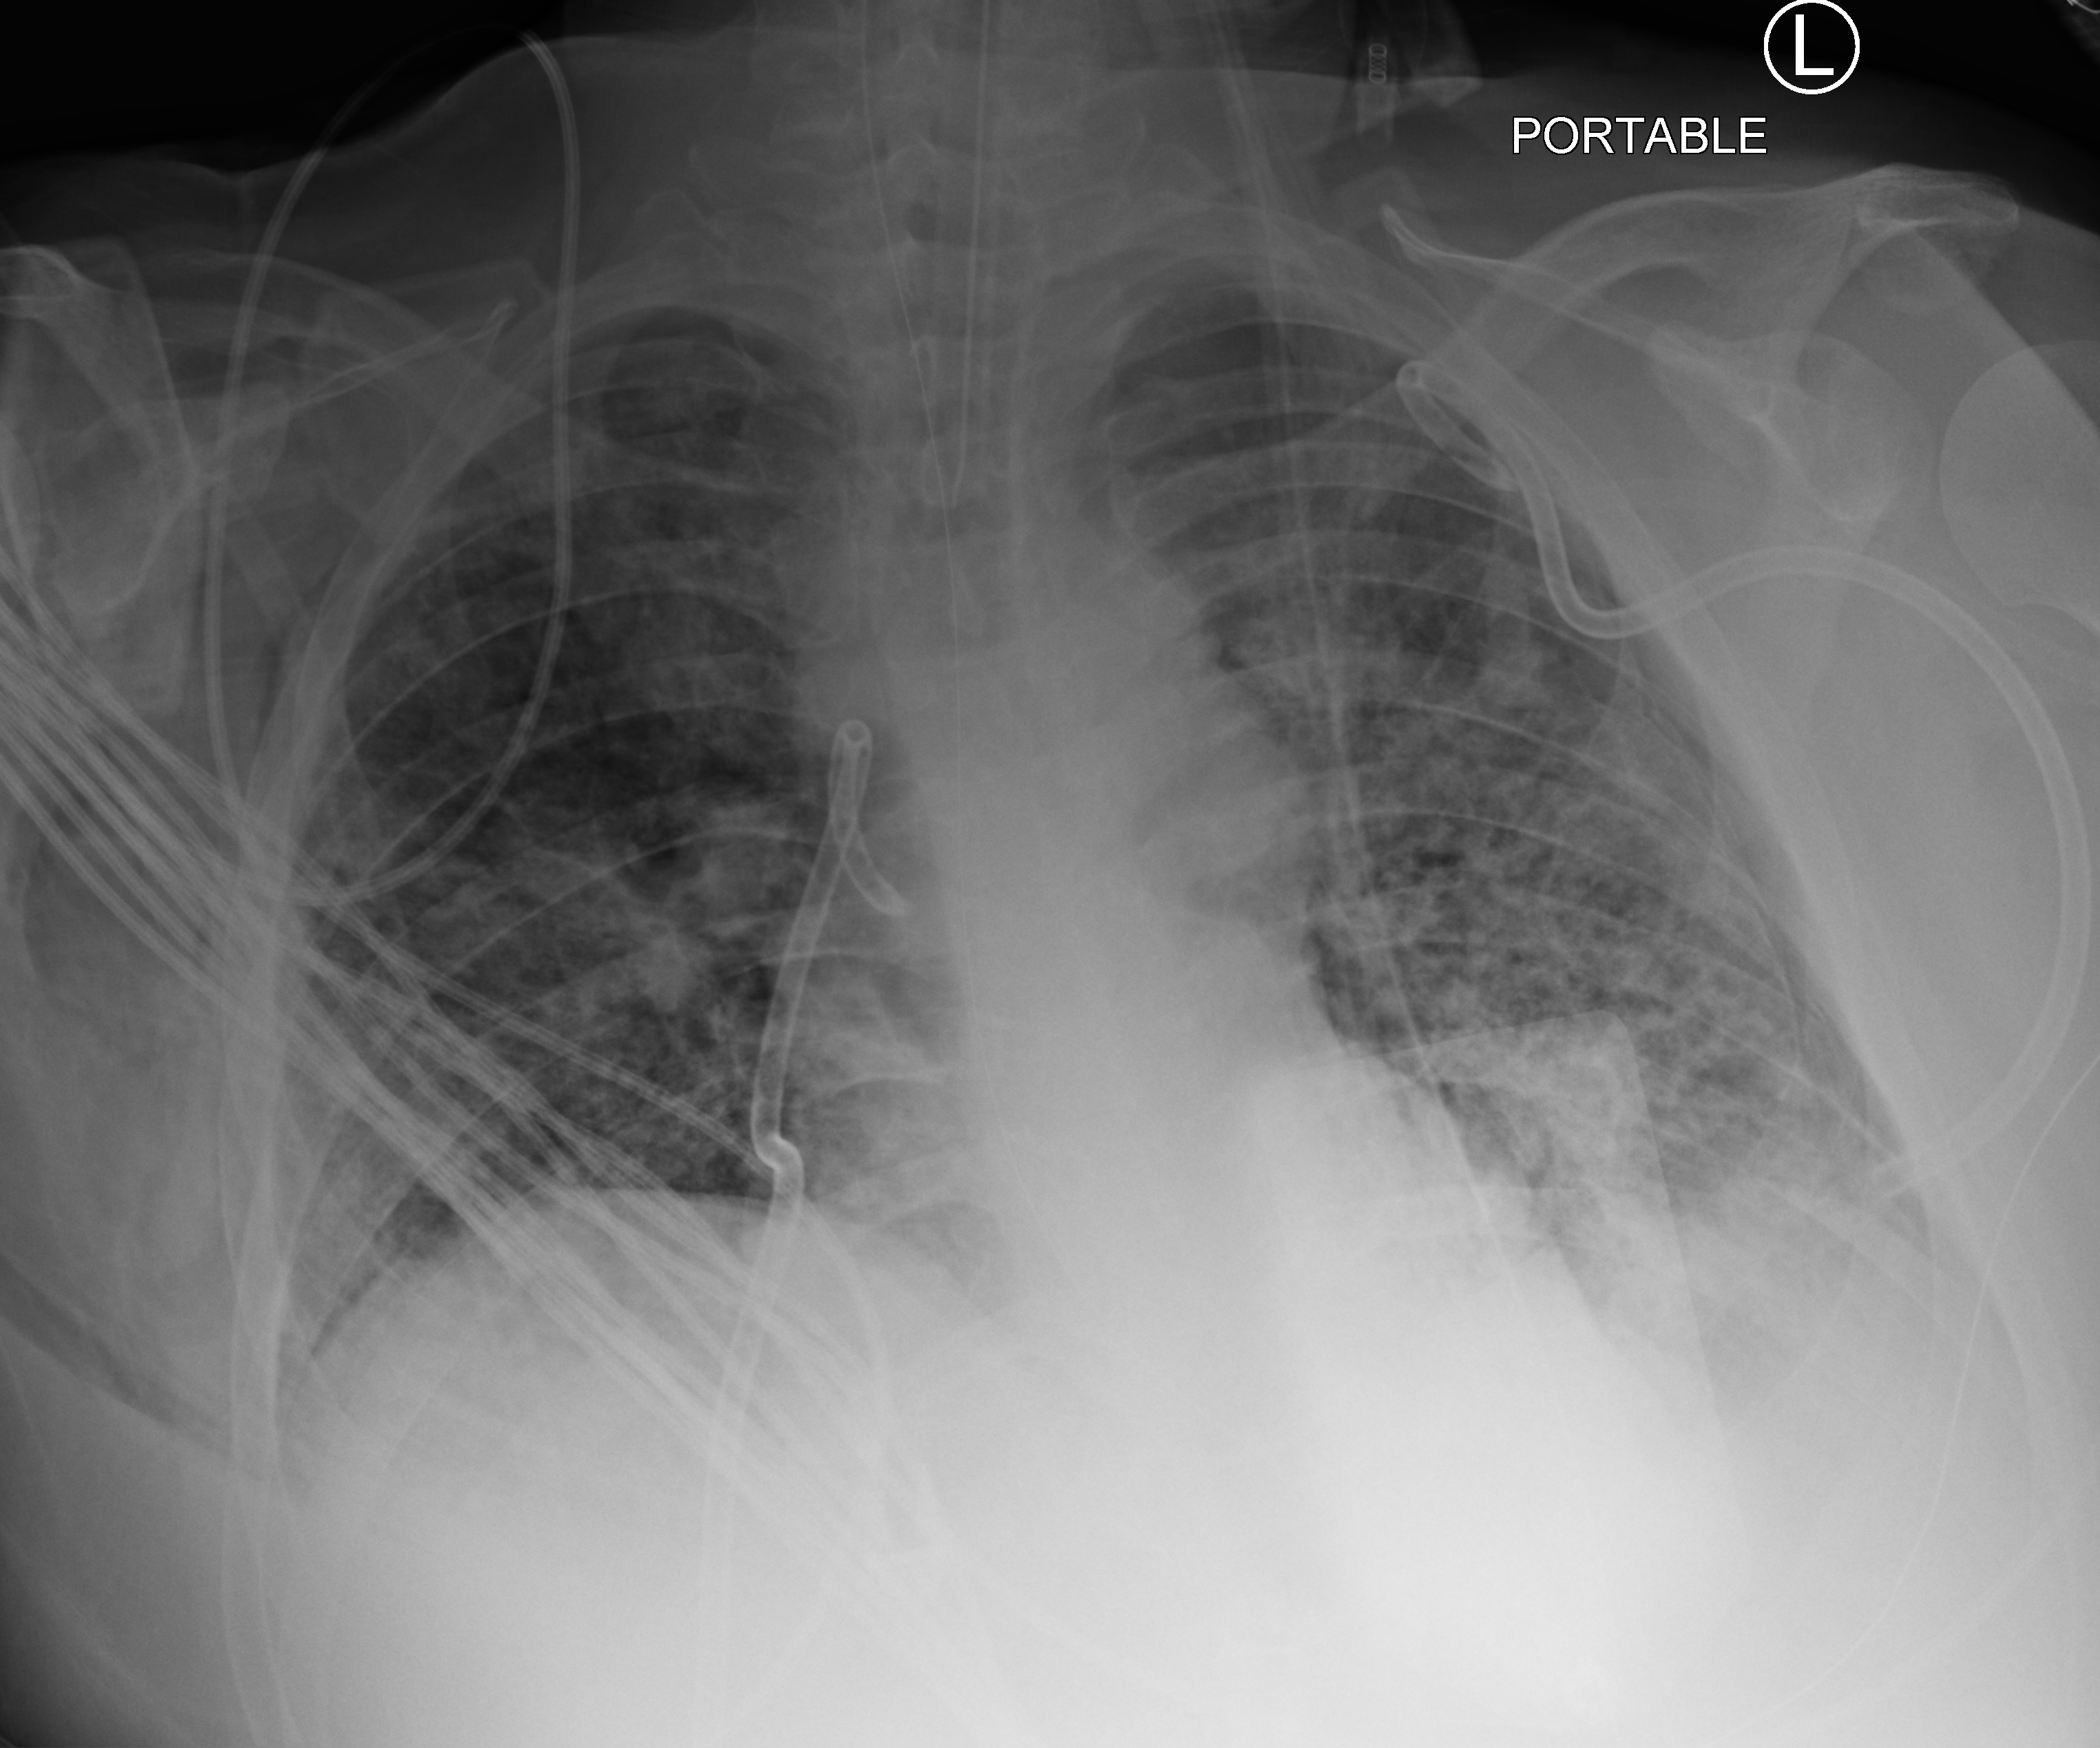
Chest X-ray (portable), anteroposterior (AP) projection. Adult patient hospitalised with COVID-19, age 18–59 years.
From the hospital-stay record, not from the radiograph (when in the stay this image was taken is not recorded):
- mechanically ventilated during this hospital stay: yes
- admitted to intensive care during this hospital stay: yes